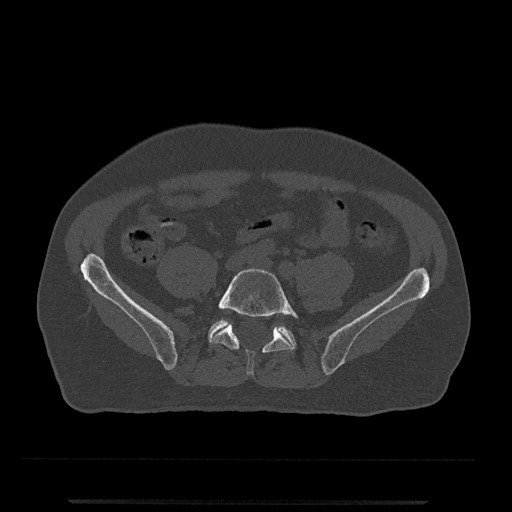
CT including the spine, one axial slice. Position 63 of 797 along the scan axis. Reconstruction kernel Br40s/3. Bone window (W 1800 / L 400 HU). 0.5 mm slice thickness. 512 × 512 image matrix, field of view 419 × 419 mm. Patient: male, 63 years. From the clinical record (not read from this slice): primary cancer: prostate.
Annotated regions visible in this slice (semi-automatically segmented with operator editing):
- L5 vertebra: bounding box (x1, y1, x2, y2) in pixels: (211, 268, 299, 376)